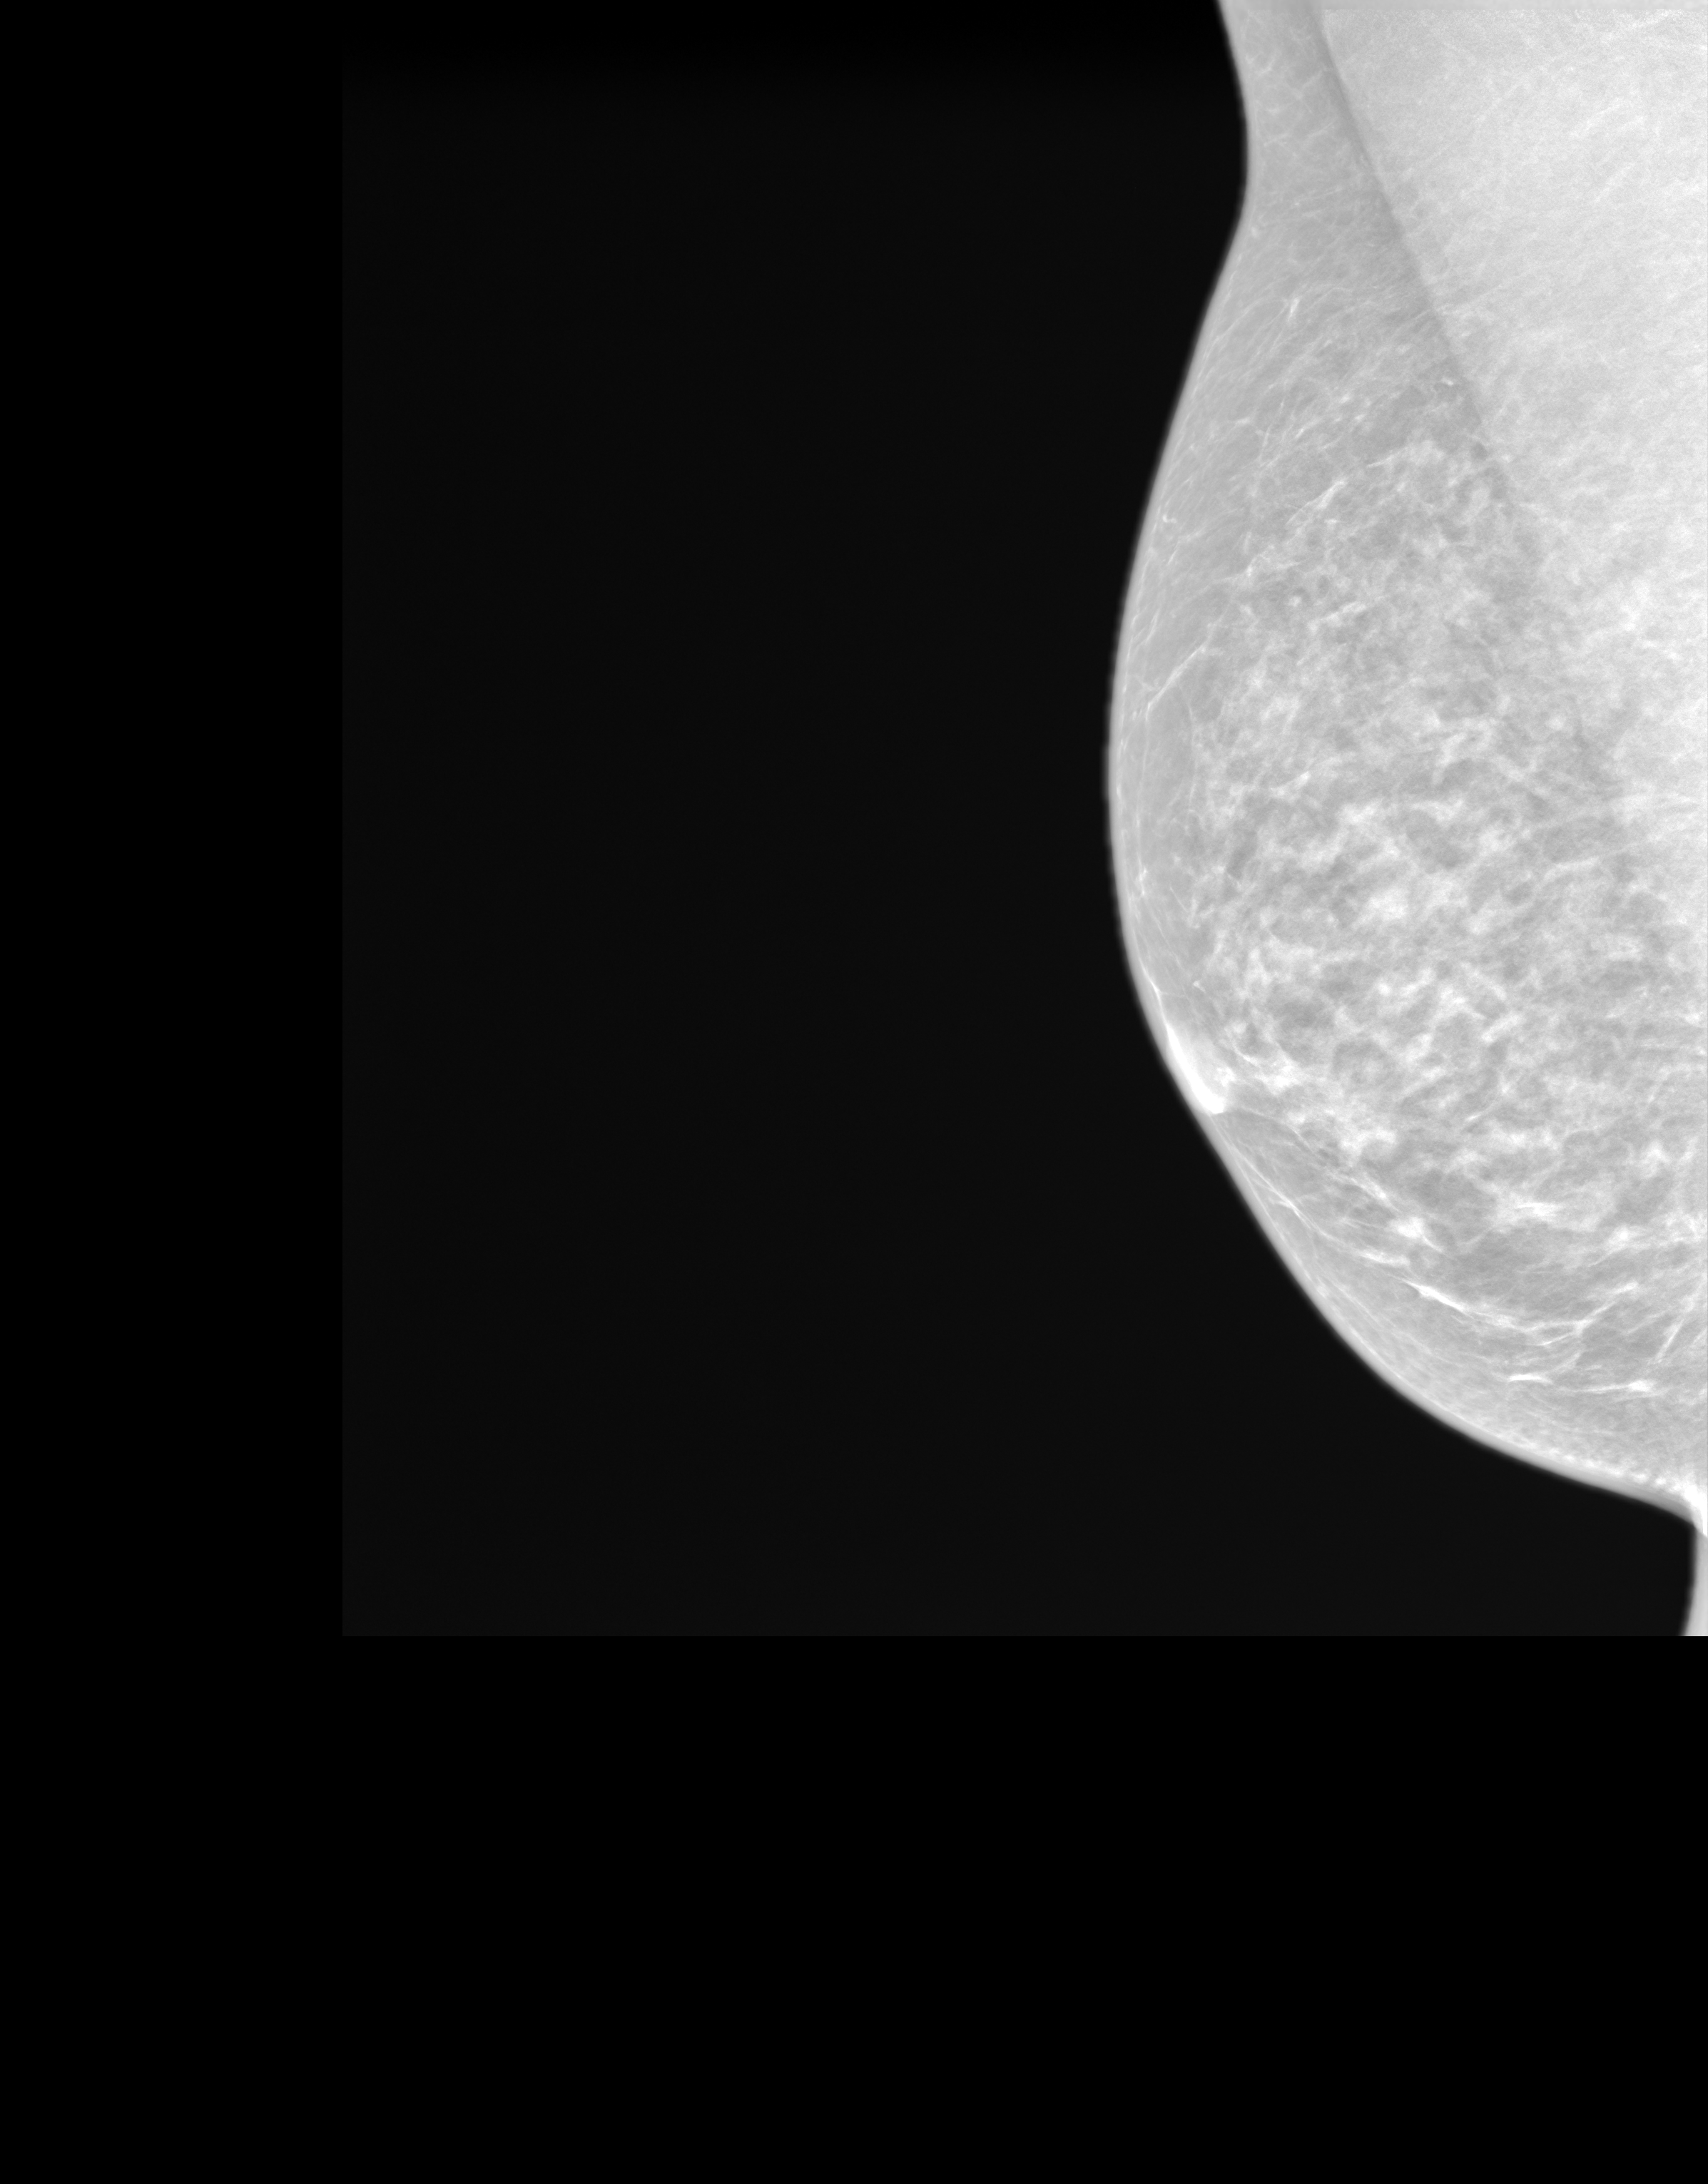
Synthesized 2-D mammogram reconstructed from digital breast tomosynthesis; right breast; MLO view; annual screening mammography examination; system: SenoIris_1SP1.1(421). Female patient, age 69 years.
- breast density at the screening exam (both breasts): heterogeneously dense (BI-RADS density category c)
- final BI-RADS category for the screening round (tomosynthesis exam, both breasts): category 1
- recall: no recall after this screen